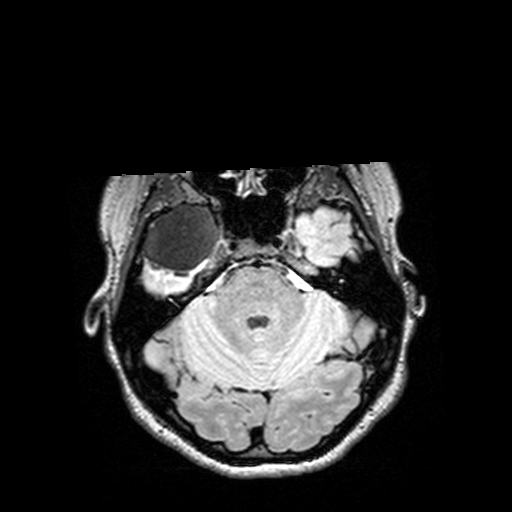
Brain MRI from a brain-tumour surgery series, one axial slice; slice 104 of 144 in the series (ordered by position); T2 FLAIR; 1 mm slice thickness; 512 × 512 image matrix. Case-level facts recorded for this patient, not image findings: histopathology: Astrocytoma; WHO grade: 3; IDH mutation: yes; tumour location: Right Insular Temporal.
Annotated regions visible in this slice (manually delineated by an expert):
- tumour: box from (x=126, y=203) to (x=232, y=277) px